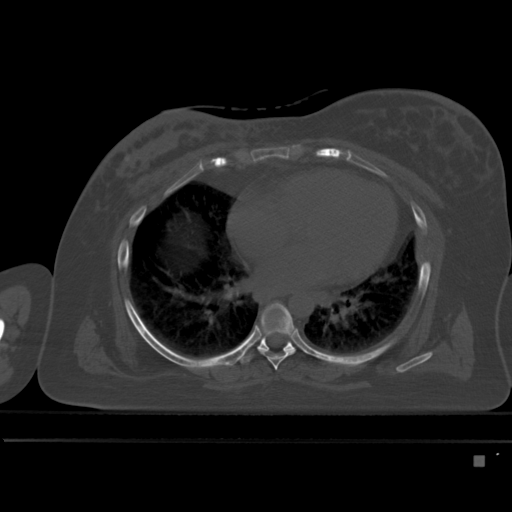
CT including the spine, one axial slice; slice 299 of 495 in the series (ordered by position); bone window (W 1800 / L 400 HU); 512 × 512 image matrix, field of view 404 × 404 mm. Female patient, age 33 years. From the clinical record (not read from this slice): primary cancer: breast; vertebrae with lytic lesions (as recorded): T1.
Outlined on this slice (semi-automatically segmented with operator editing):
- T6 vertebra: bounding box [x1, y1, x2, y2] px = [258, 304, 296, 370]
- T7 vertebra: [243, 329, 294, 363]